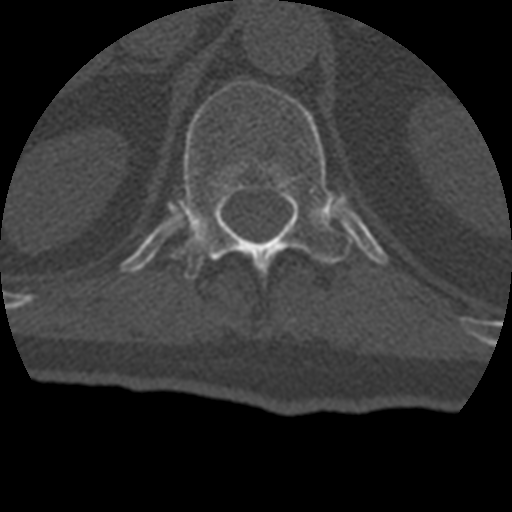
CT including the spine, one axial slice. Position 173 of 399 along the scan axis. Reconstruction kernel STANDARD. 120 kVp. Bone window (W 1800 / L 400 HU). 512 × 512 image matrix. Patient age 69 years. From the clinical record (not read from this slice): primary cancer: prostate.
Outlined on this slice (semi-automatically segmented with operator editing):
- T12 vertebra: bounding box [x1, y1, x2, y2] px = [175, 81, 352, 278]